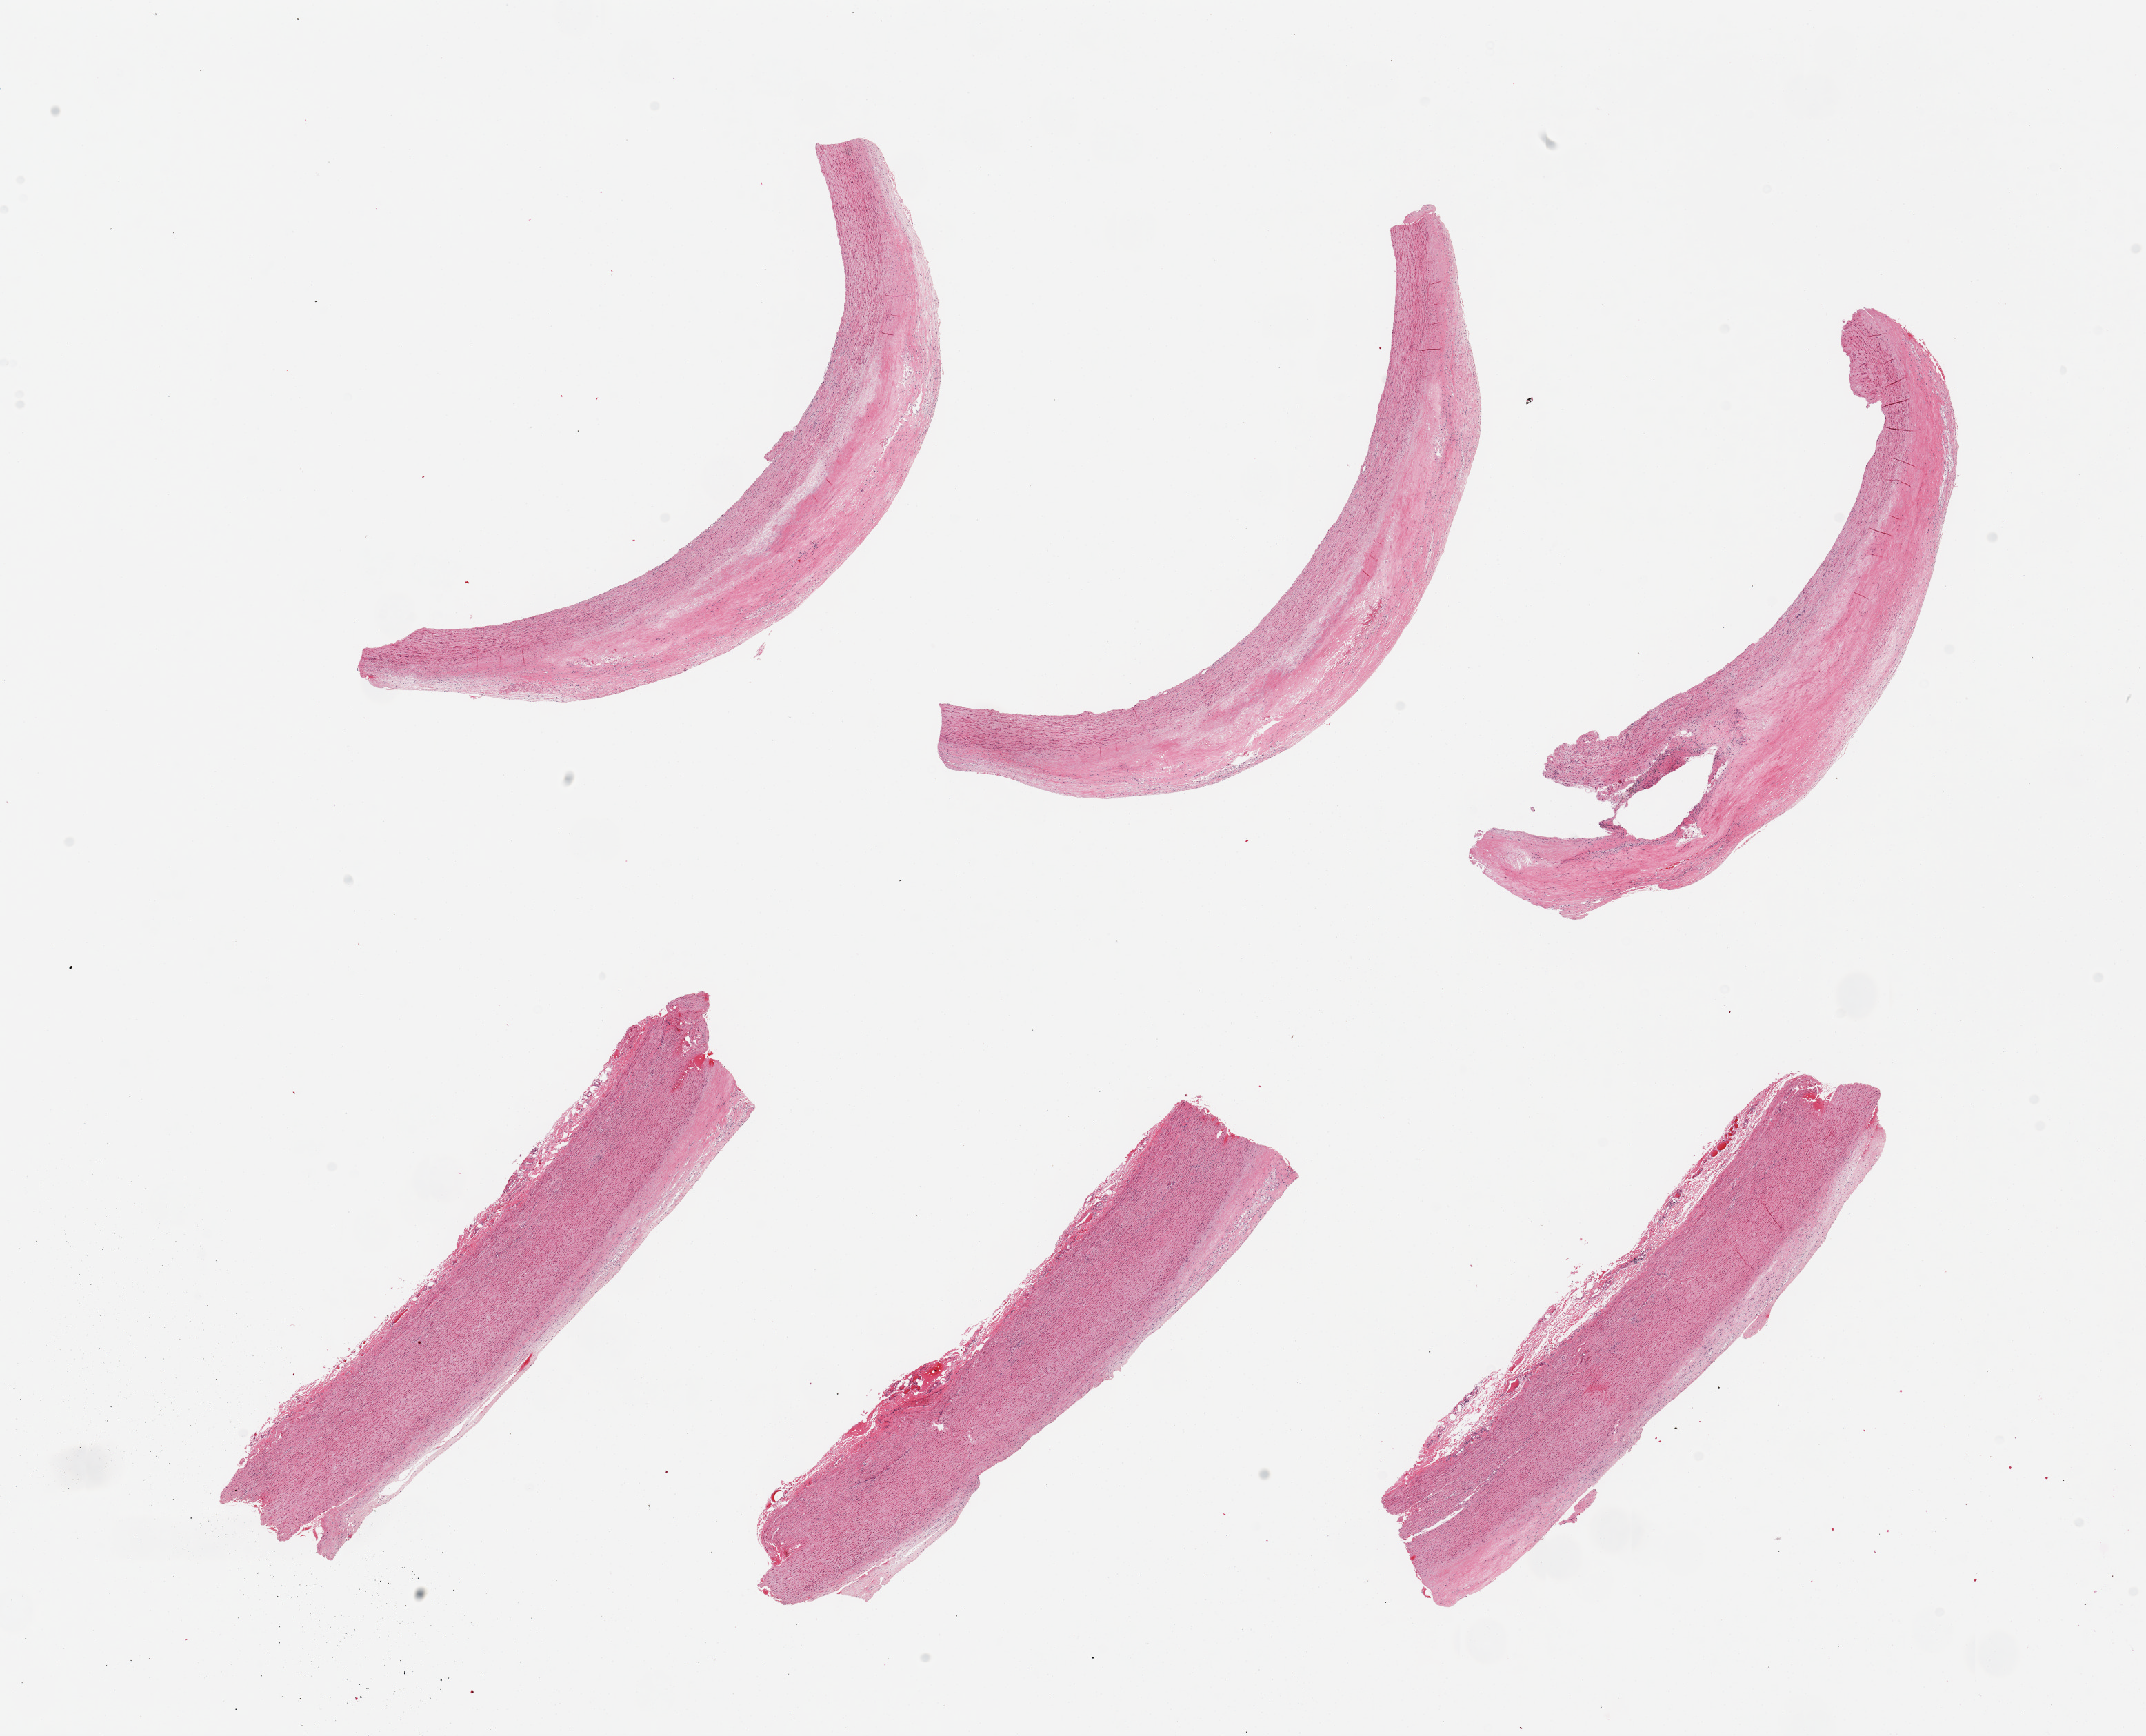
Digitized H&E-stained section, brightfield, shown as a low-resolution overview of the whole scanned area (about 24.6 x 19.9 mm, from a 20x scan); PAXgene-fixed, paraffin-embedded tissue; section of aorta (target tissue); donor tissue sample.
Review note (as recorded): 6 pieces; atherosclerotic plaque.